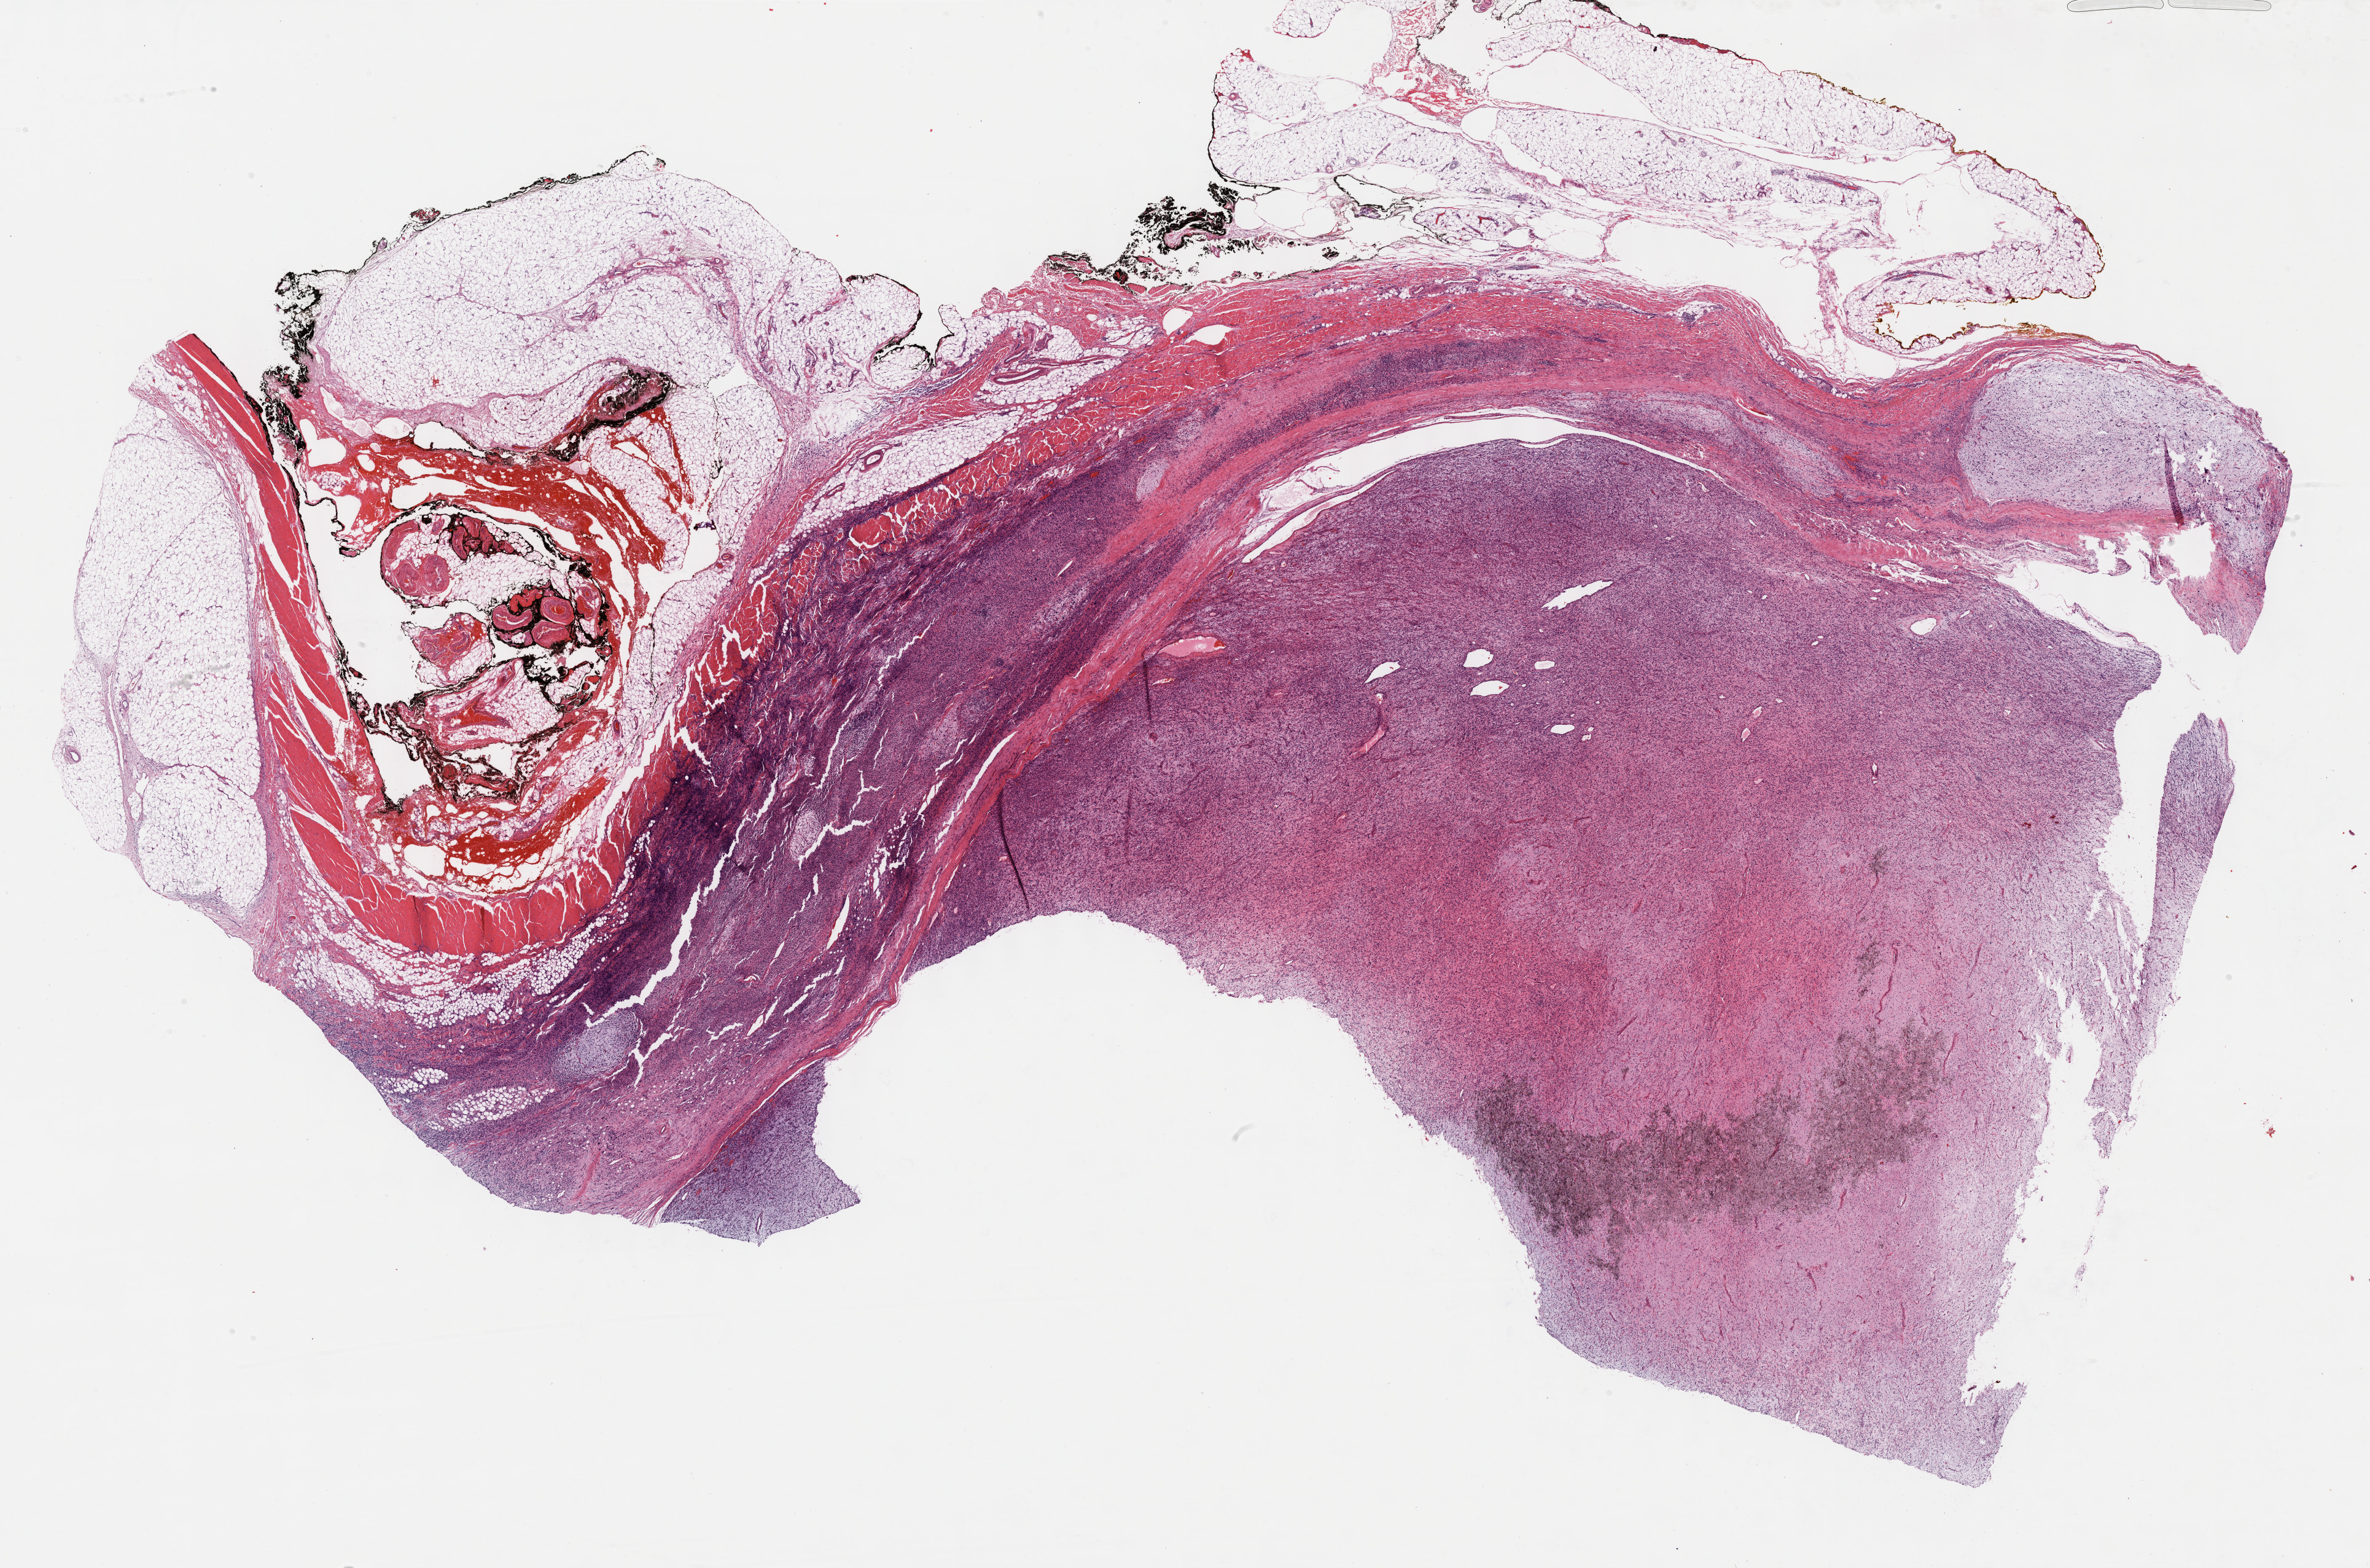
H&E-stained whole-slide image — a low-resolution overview of the entire scanned area, about 31.2 x 20.6 mm (slide scanned at 40x), formalin-fixed paraffin-embedded (FFPE) diagnostic section, sample: primary tumour, connective, subcutaneous and other soft tissues. Male, age 35 years at initial diagnosis.
- diagnosis: Fibromyxosarcoma (connective, subcutaneous and other soft tissues of lower limb and hip)